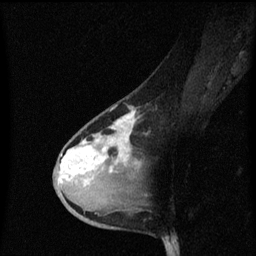
Breast MRI (dynamic contrast-enhanced), one sagittal slice; slice 36 of 60 in the series (ordered by position); dynamic contrast-enhanced series, image 2 of 3 at this slice position (ordered by acquisition); 1.5 T; TE 4.2 ms, TR 8.4 ms; 2 mm slice thickness; 256 × 256 image matrix, field of view 200 × 200 mm. Patient: female, 38 years. Case-level facts recorded for this patient, not image findings: setting: breast cancer imaged before/during neoadjuvant chemotherapy; receptor status: HR-positive, HER2-negative.
Outlined on this slice (semi-automatically segmented with operator editing):
- analysis volume of interest (the breast-tissue region the enhancement analysis was run in; not a lesion): bounding box (x1, y1, x2, y2) in pixels: (54, 102, 147, 205)
- tumour enhancement mask (voxels above the 70 % enhancement threshold inside the analysis volume of interest): (60, 112, 139, 183)